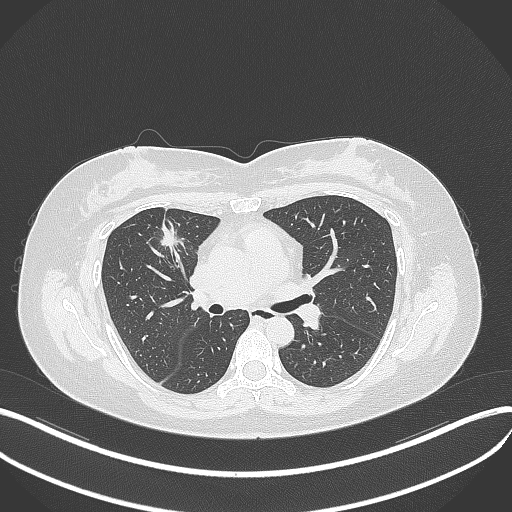
Chest CT, one axial slice; position 187 of 273 along the scan axis; reconstruction kernel B70f; 120 kVp; lung window (W 1500 / L -600 HU); 1 mm slice thickness; 512 × 512 image matrix, field of view 400 × 400 mm. Female patient, age 42 years. Case-level facts recorded for this patient, not image findings: clinical TNM (as recorded): T1b N0 M0.
Structures marked on this image (rectangle marked by the reading radiologist):
- lung tumour (recorded histology: adenocarcinoma): bounding box <155,220,181,249> (left, top, right, bottom; pixels)